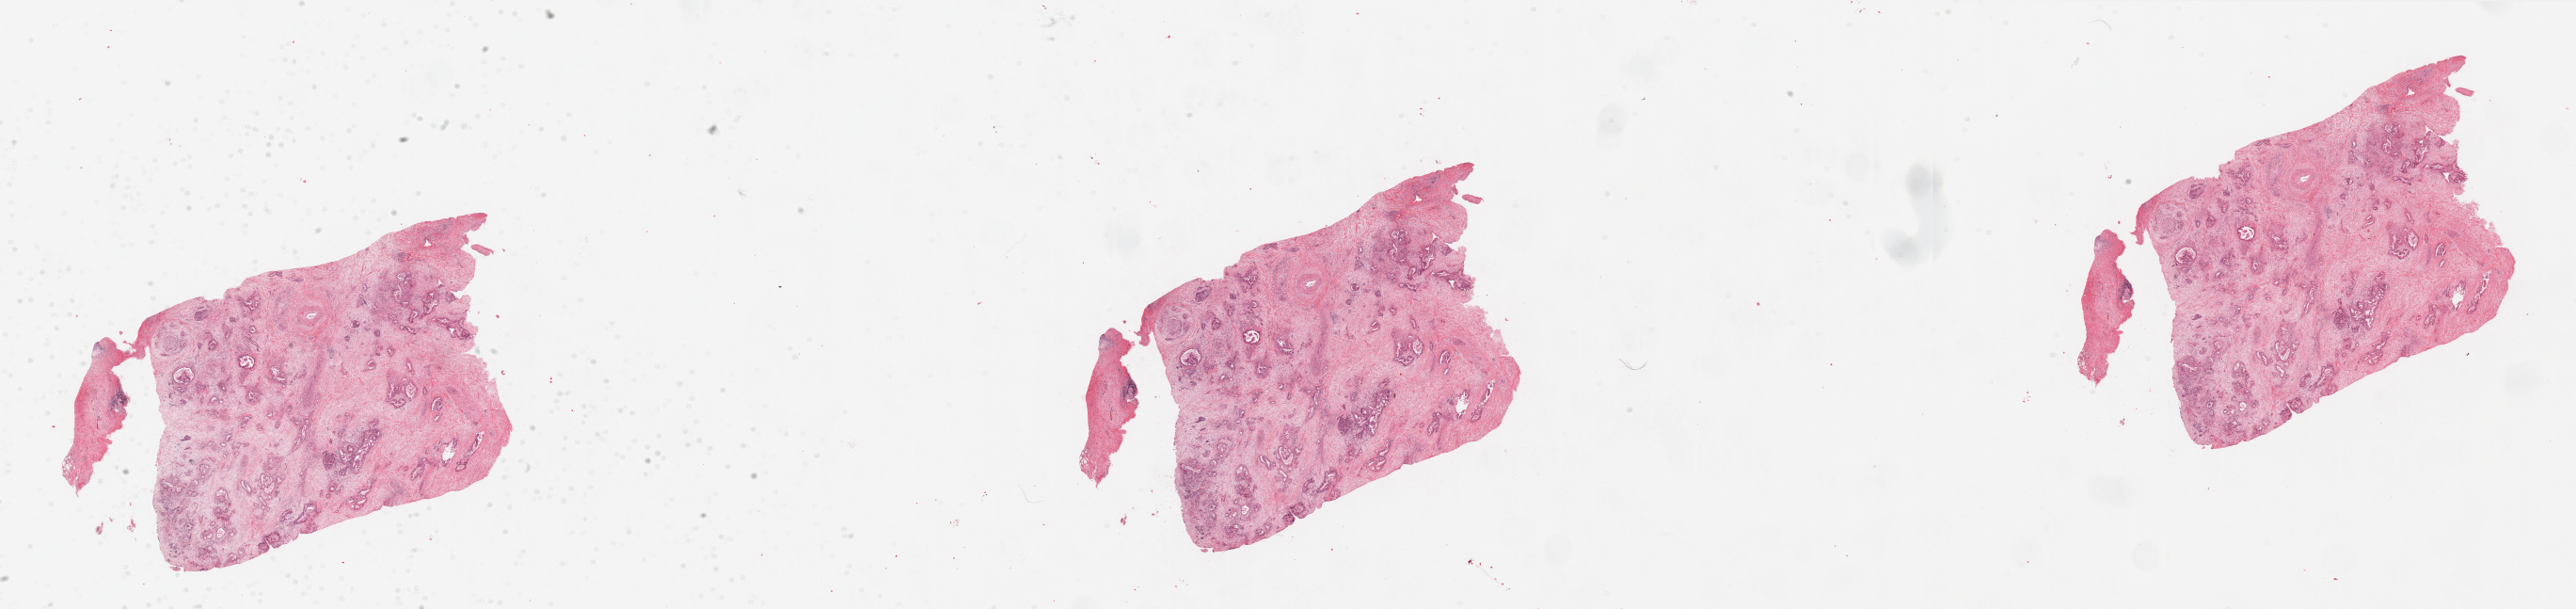
Hematoxylin and eosin (H&E) stained whole-slide image, whole scanned area (about 43.3 x 10.2 mm, slide scanned at 20x) shown as a low-resolution overview. Tumour tissue sample, pancreas. Male, 55 y/o. Histologic grade: G2 (moderately differentiated).
Histologic diagnosis: Infiltrating duct carcinoma, NOS. Primary tumour site (as recorded): body. AJCC pathologic stage: IIB.